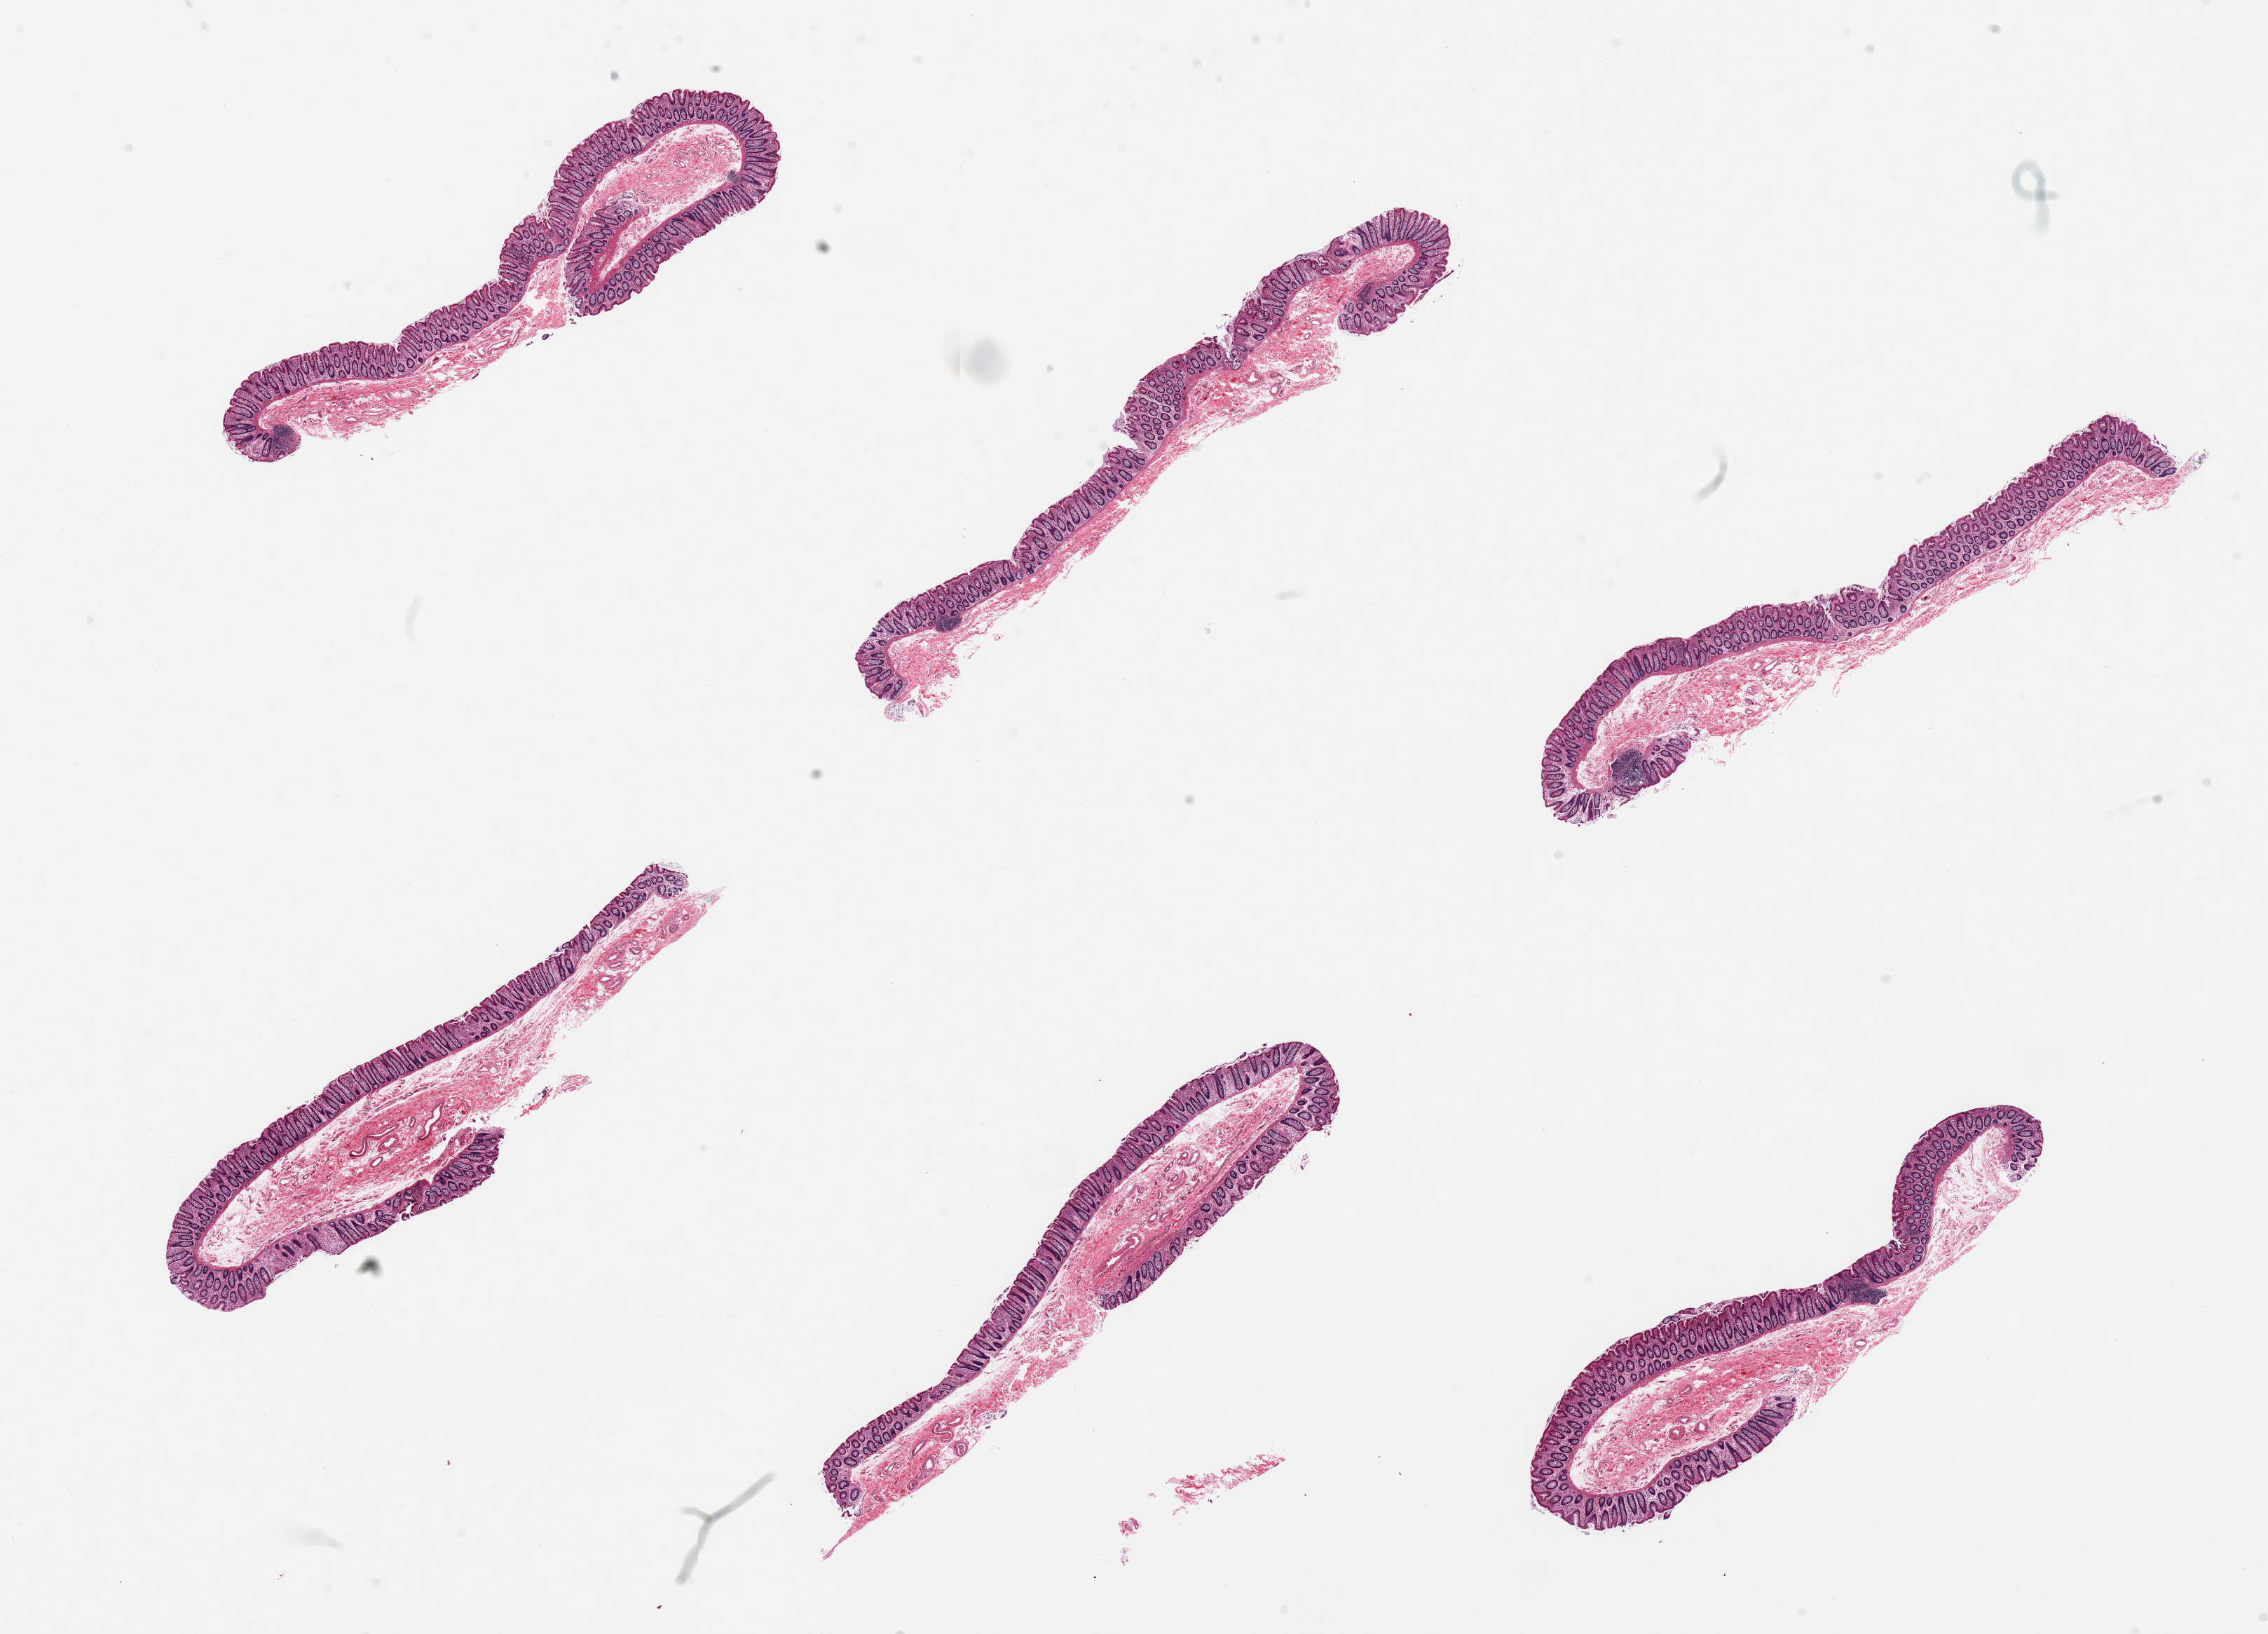
Digitized haematoxylin and eosin-stained section, brightfield — a low-resolution overview of the entire scanned area, about 25.6 x 18.4 mm (from a 20x scan). PAXgene-fixed, paraffin-embedded tissue. Sampled site (target tissue): transverse colon. Tissue donor sample. Donor sex: male.
Review note (as recorded): 6 pieces, well preserved mucosa up to ~40-50% thickness.